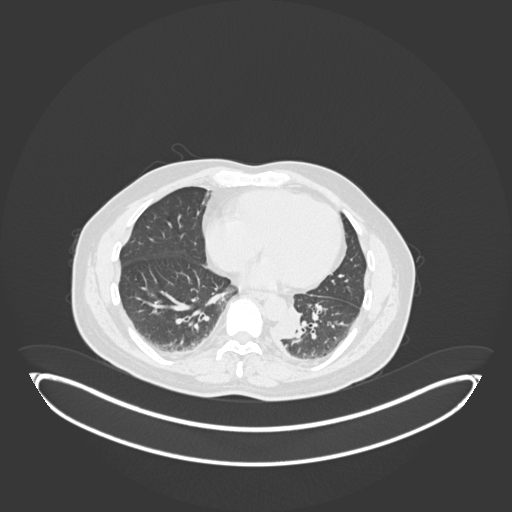
Chest CT, one axial slice. 120 kVp. Lung window (W 1500 / L -600 HU). 1 mm slice thickness. 512 × 512 image matrix. Male patient, age 54 years. From the clinical record (not read from this slice): clinical TNM (as recorded): T3 N0 M0.
Outlined on this slice (rectangle marked by the reading radiologist):
- lung tumour (recorded histology: squamous cell carcinoma): bounding box <277,306,307,347> (left, top, right, bottom; pixels)